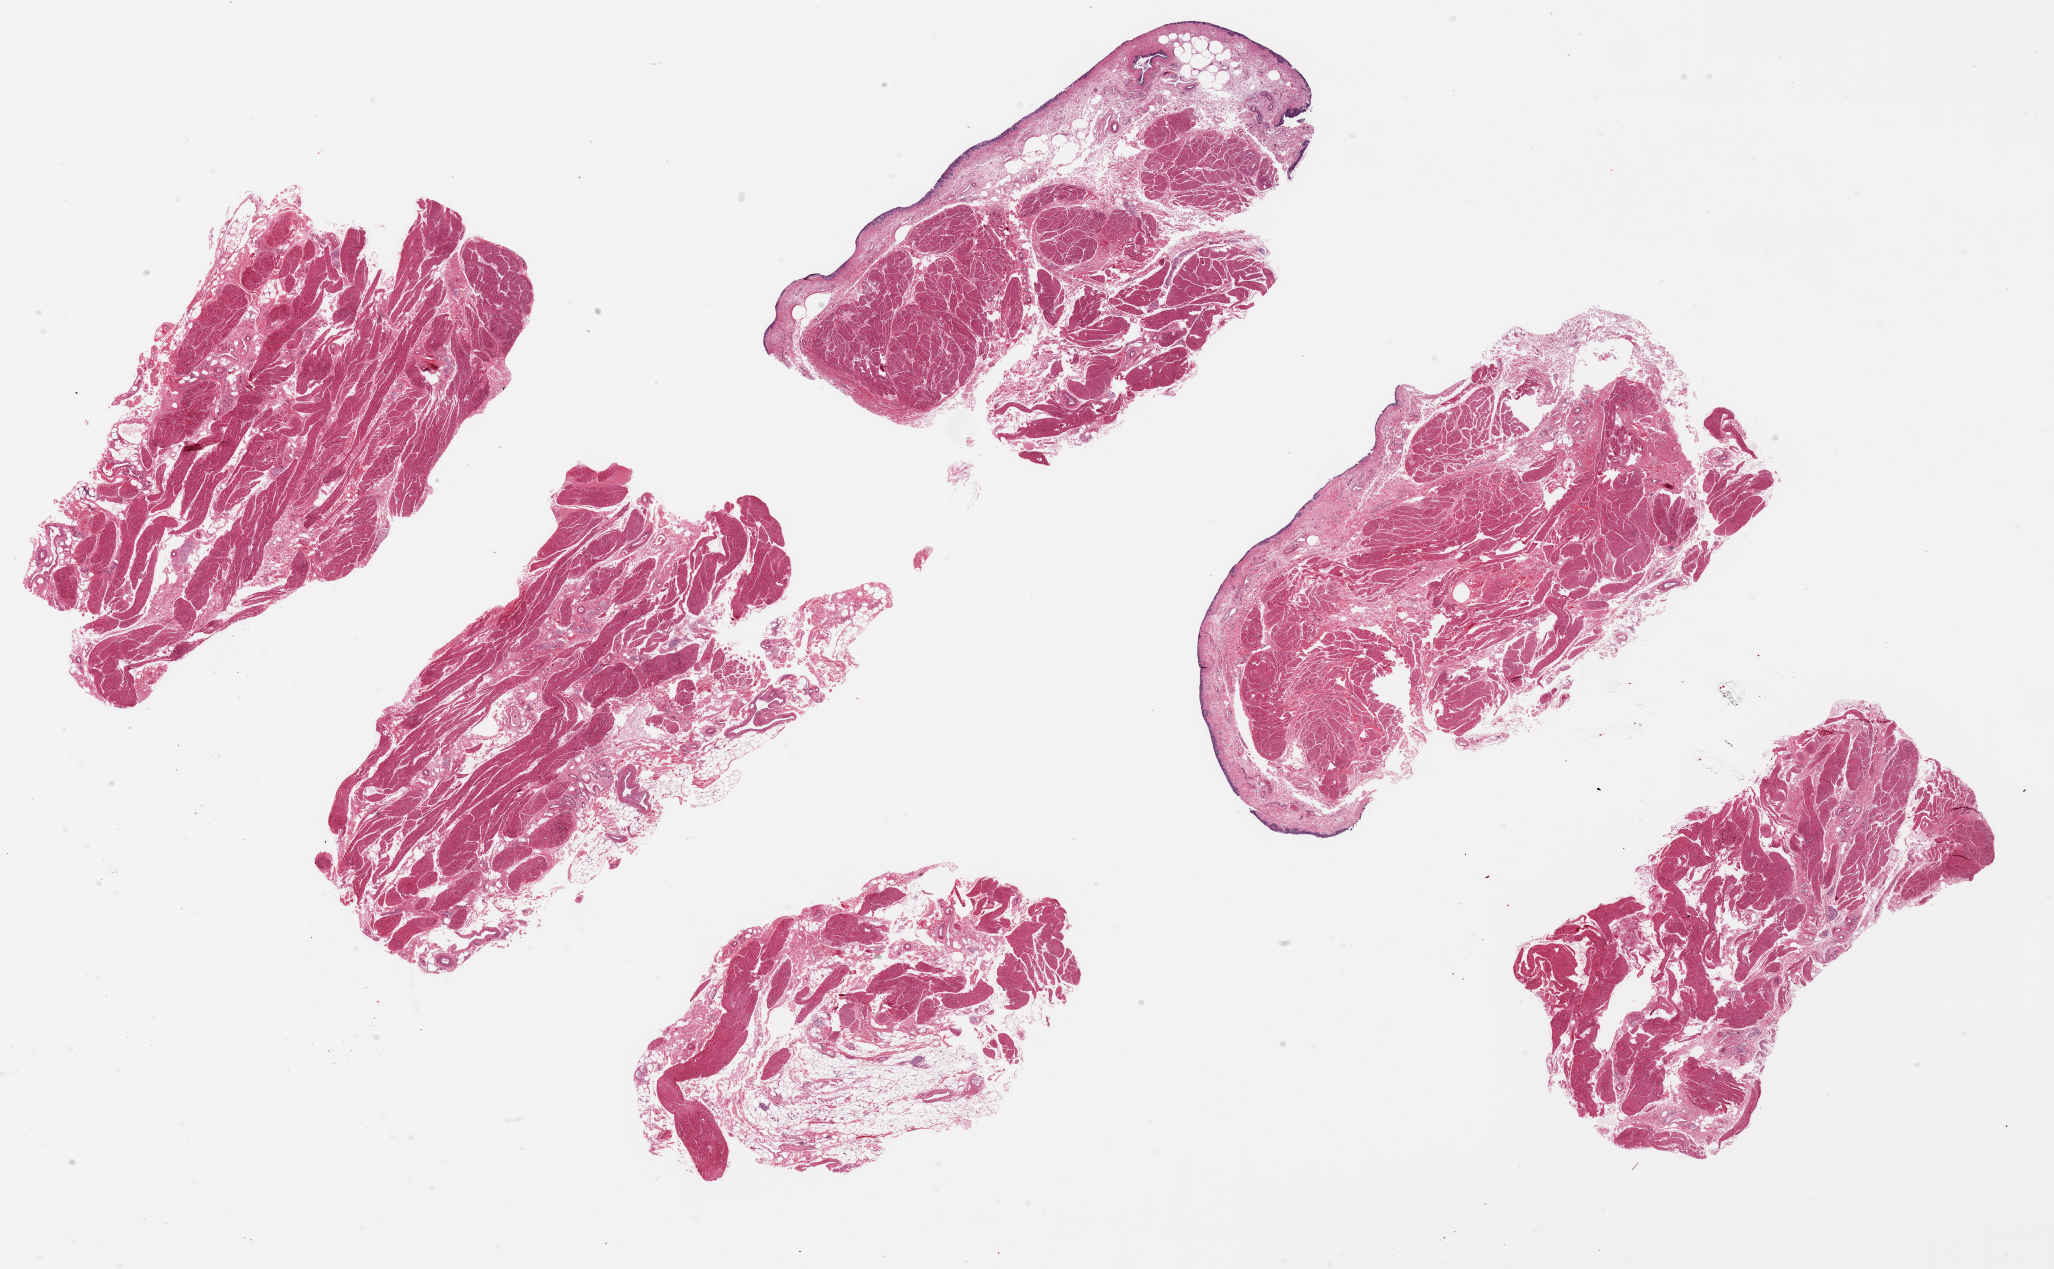
Whole-slide image, hematoxylin and eosin (H&E) stain, brightfield — shown as a low-resolution overview of the whole scanned area (about 32.5 x 20.1 mm, slide scanned at 20x). PAXgene-fixed paraffin-embedded (PFPE) section. Section of urinary bladder (target tissue). Tissue donor sample. Male donor.
- review note (as recorded): 6 ~9x4mm pieces. Urothelium largely denuded/sloughed. Areas of poor fixation with holes/tears